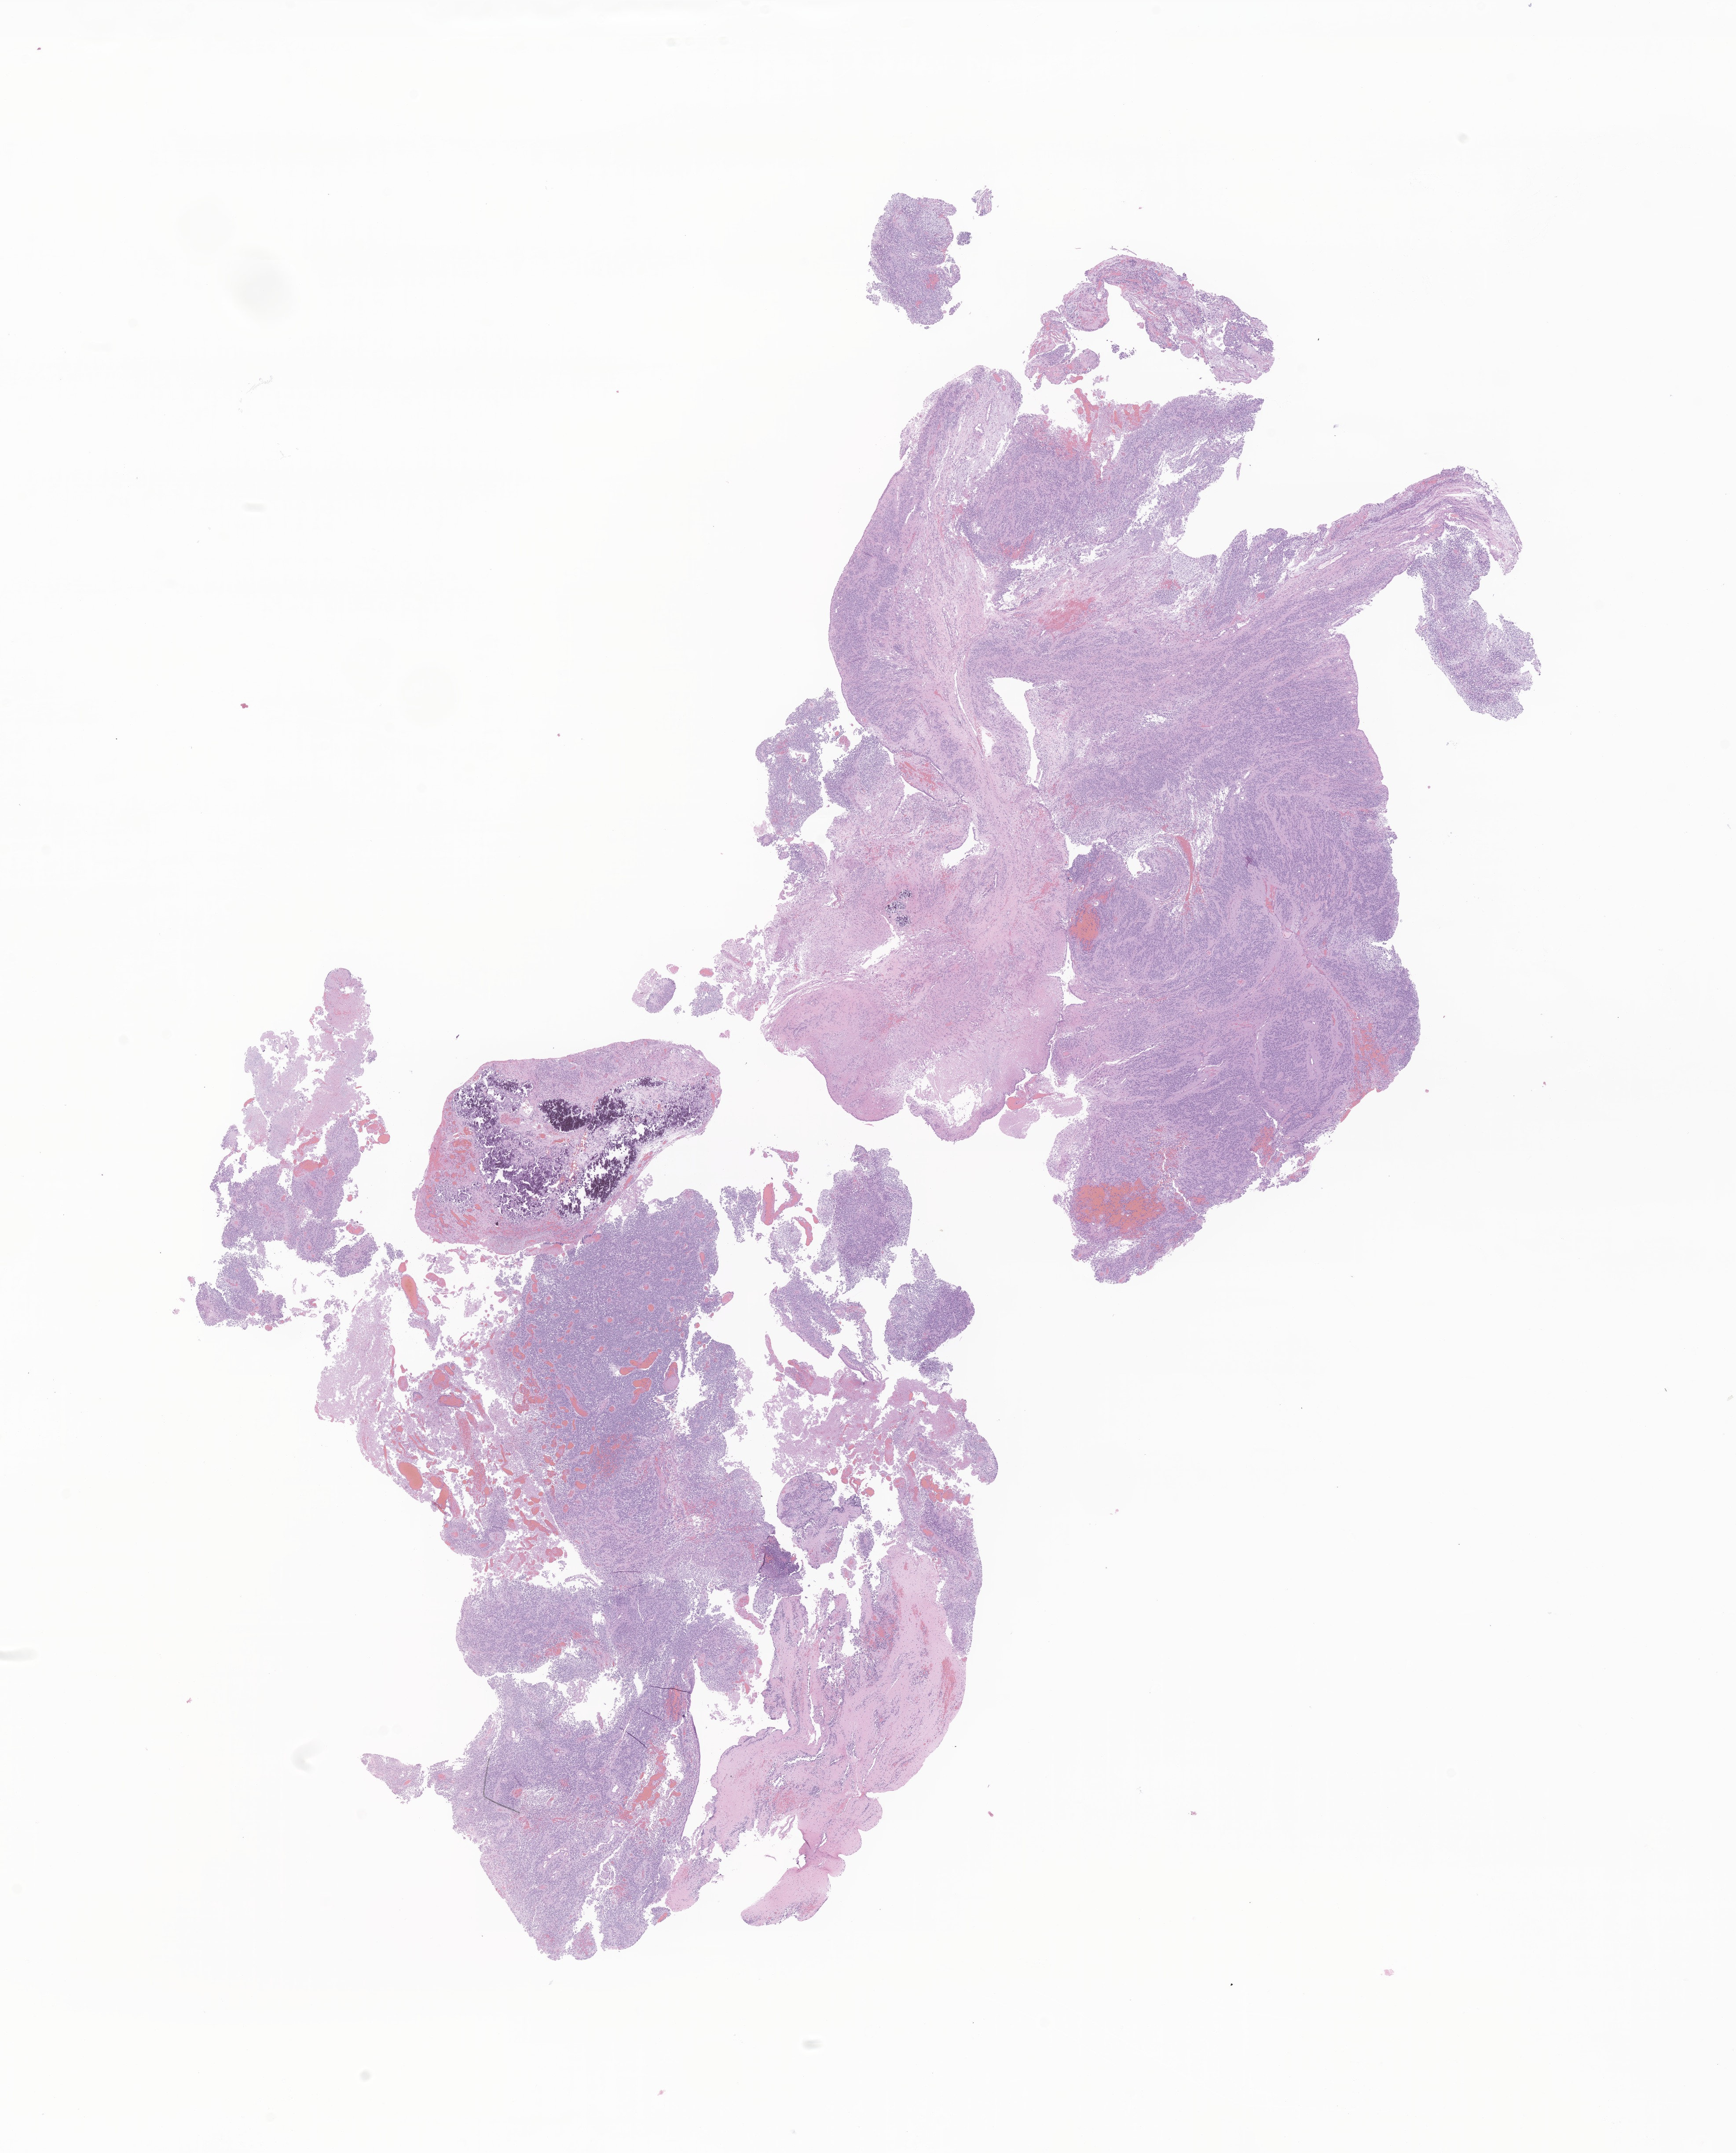
Whole-slide image, hematoxylin and eosin (H&E) stain of tumor tissue from the brain, whole scanned area (about 16.6 x 20.6 mm) shown as a low-resolution overview, formalin-fixed paraffin-embedded section. Patient male; age 57 months (4 years 9 months).
Diagnosis (ICD-O-3 morphology term): Ependymoma, NOS.